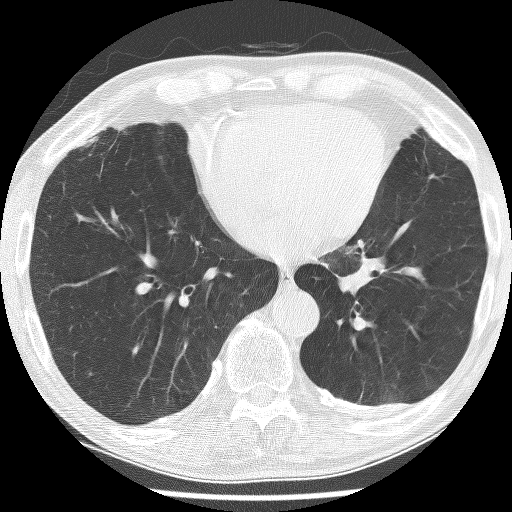
Chest CT (low-dose screening protocol), one axial image, first (baseline) screen, lung window (W 1500 / L -600 HU), 2.5 mm slice thickness, lung (sharp) reconstruction kernel (BONE), slice 163 of 226 in the series, 512 × 512 image matrix. Male participant, aged 74 years at enrolment. Current smoker at enrolment.
Expert reader's lesion annotation, bounding box (x1, y1, x2, y2) in pixels: (320, 233, 430, 327). Screening reader's record for this exam (one nodule recorded; not confirmed to be the boxed lesion): non-calcified nodule or mass ≥4 mm, left lower lobe, 30 × 27 mm, spiculated (stellate) margins, soft tissue attenuation. Later outcome: lung cancer diagnosed 151 days after this screen — adenocarcinoma, NOS, left lower lobe, stage IIIA (AJCC 6th edition), 49 mm at pathology.